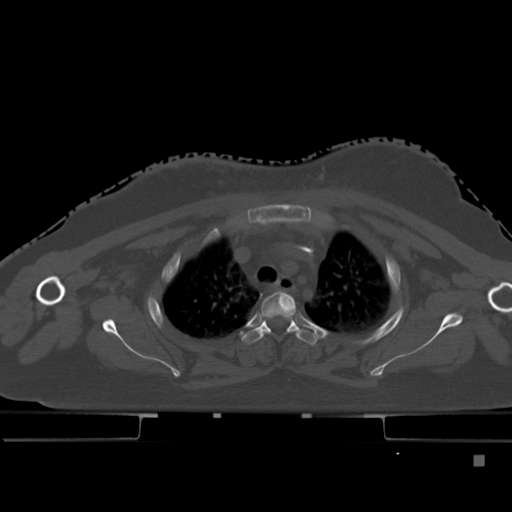
CT including the spine, one axial slice; slice 351 of 495 in the series (ordered by position); bone window (W 1800 / L 400 HU); 1.5 mm slice thickness; 512 × 512 image matrix, field of view 404 × 404 mm. Patient: female, 33 years. Case-level facts recorded for this patient, not image findings: primary cancer: breast; vertebrae with lytic lesions (as recorded): T1.
Outlined on this slice (semi-automatically segmented with operator editing):
- T2 vertebra: bounding box [x1, y1, x2, y2] px = [261, 291, 296, 331]
- T3 vertebra: [241, 318, 319, 345]